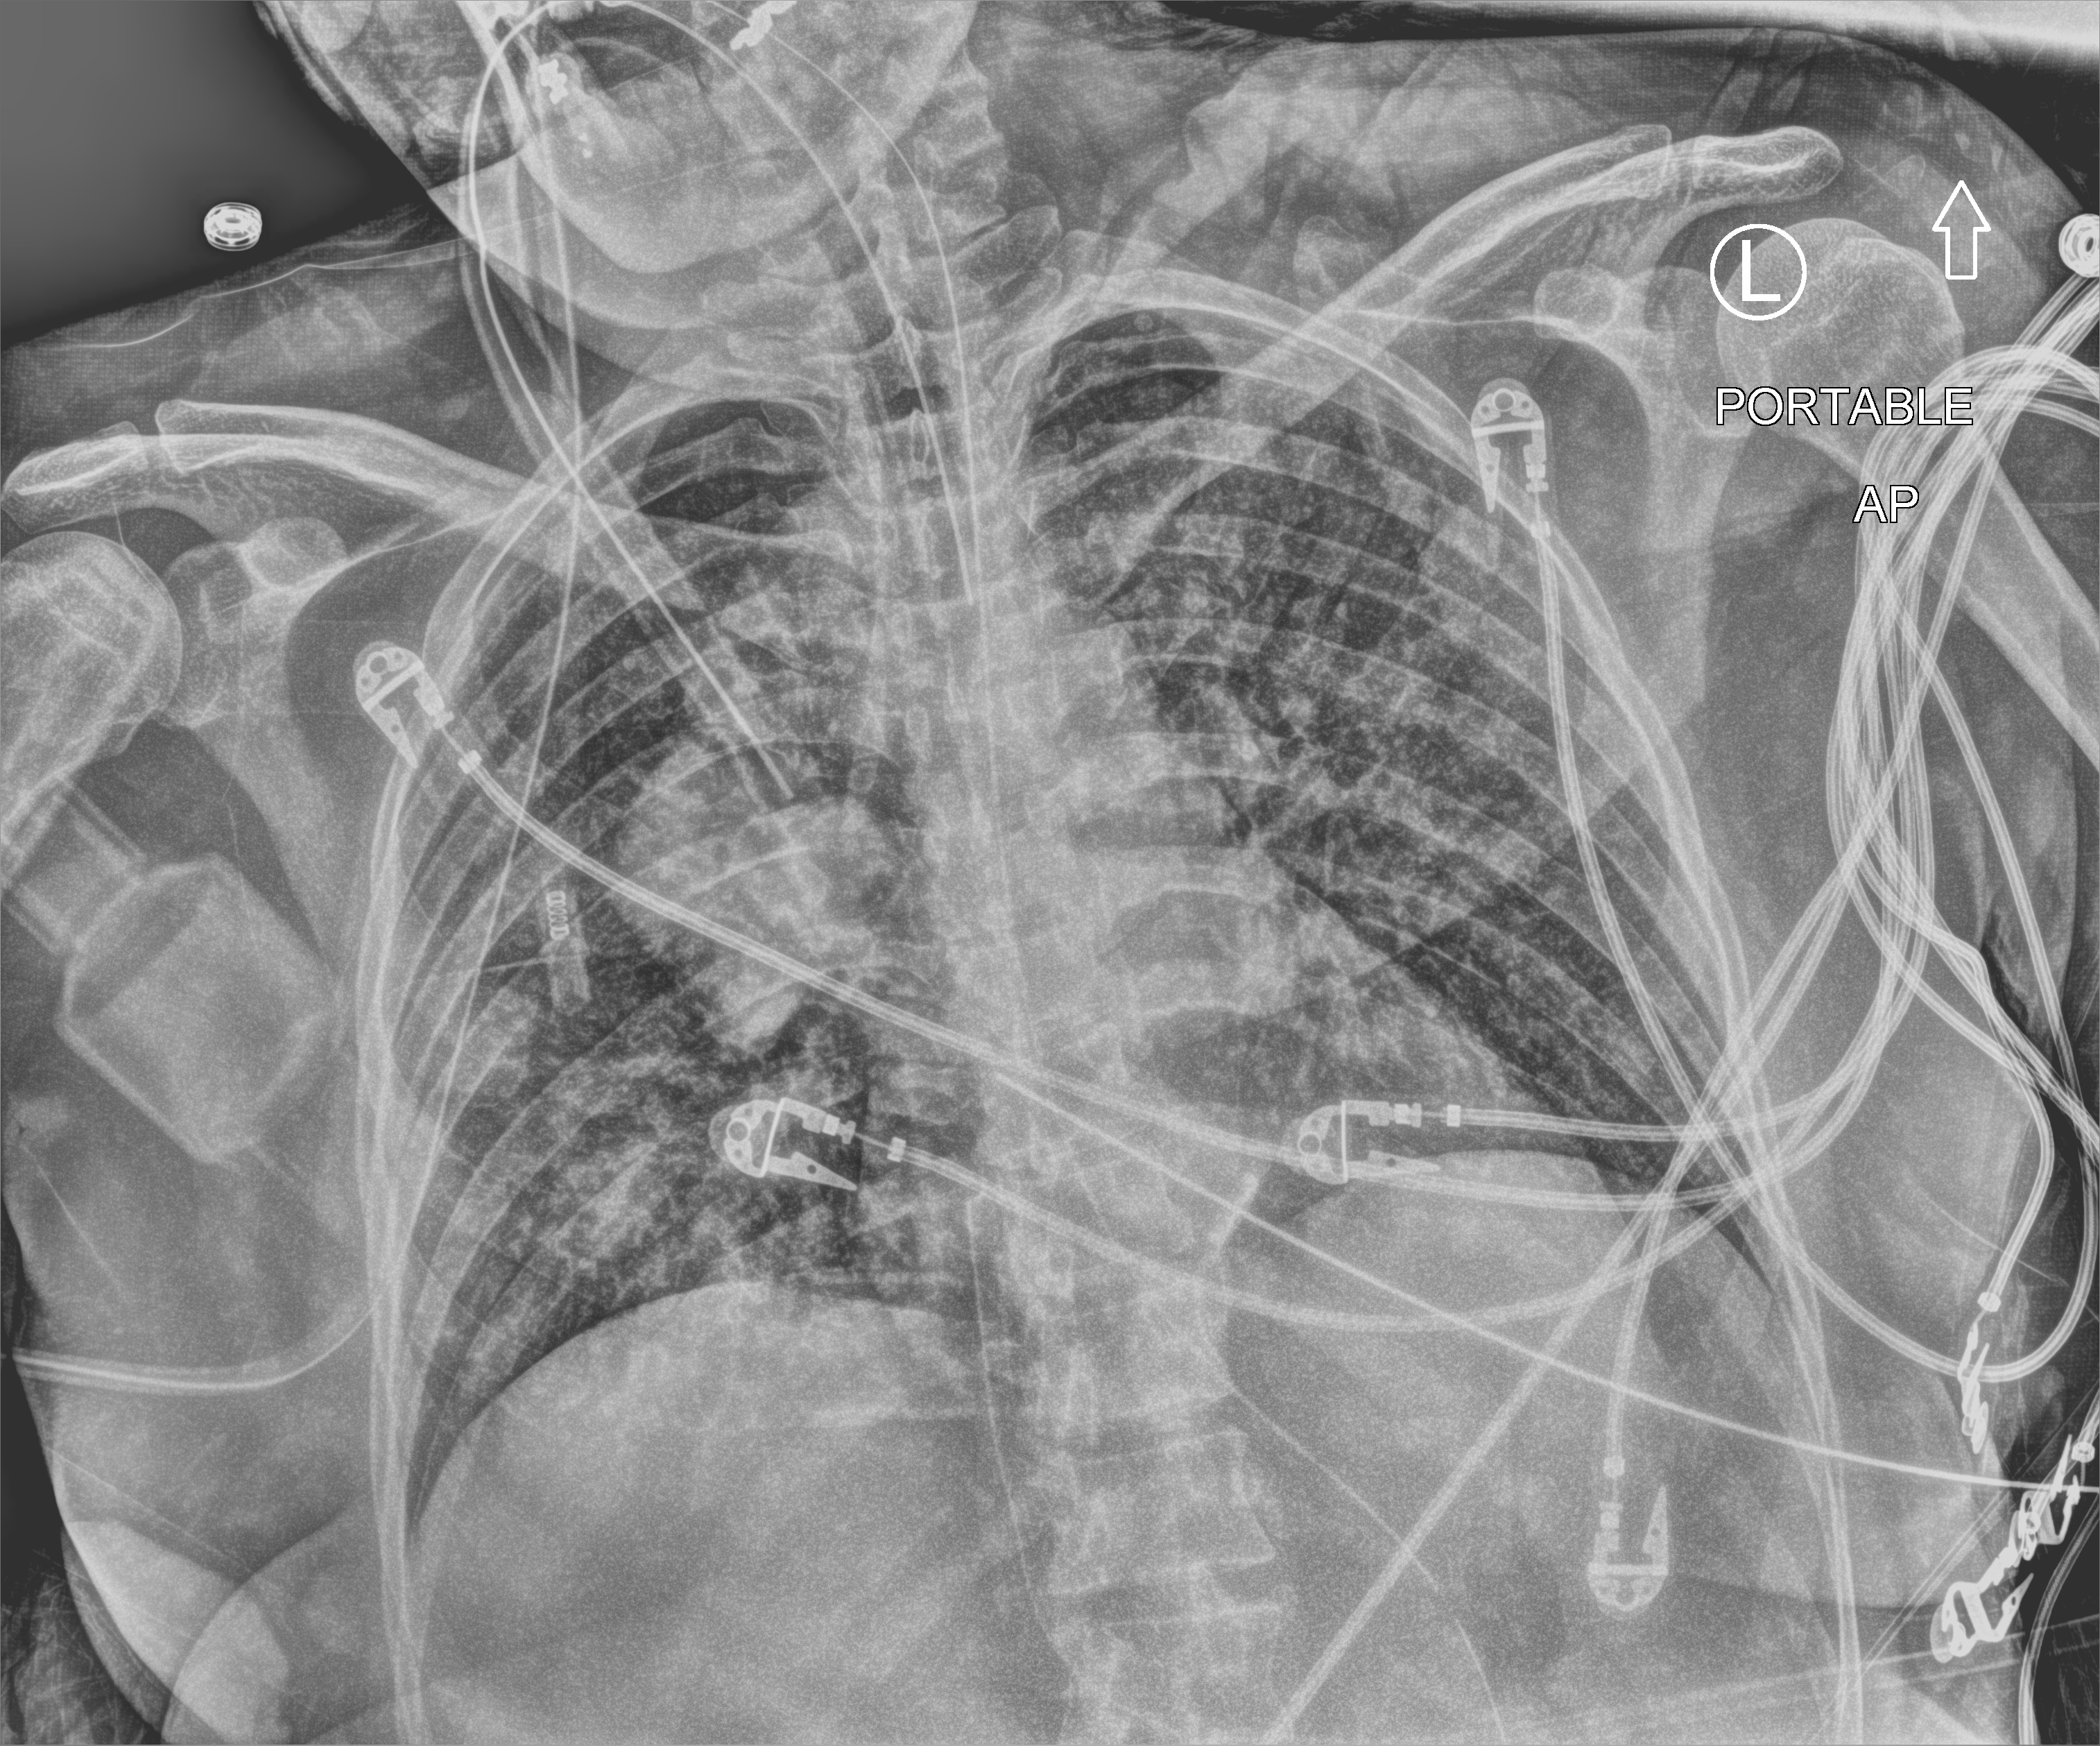
Portable chest radiograph, anteroposterior (AP) projection. Female patient hospitalised with COVID-19, age 18–59 years.
Hospital-stay facts (about this admission, not read from this image; timing relative to this image not recorded): admitted to intensive care during this hospital stay: yes.